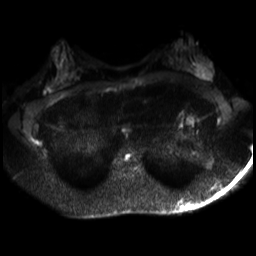
Breast MRI, one axial slice; position 16 of 30 along the scan axis; diffusion-weighted series; image 2 of 4 stored at this slice position (different b-values; order by instance number); 3 T; 4 mm slice thickness; 256 × 256 image matrix, field of view 320 × 320 mm. Female patient.
Outlined on this slice (manually delineated by an expert):
- tumour on diffusion-weighted imaging: bounding box (x1, y1, x2, y2) in pixels: (198, 65, 206, 78)